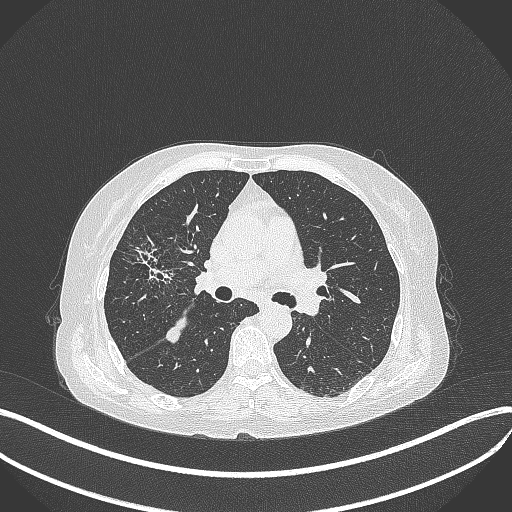
Chest CT, one axial slice; 120 kVp; lung window (W 1500 / L -600 HU); 1 mm slice thickness; 512 × 512 image matrix. Female patient, age 69 years. From the clinical record (not read from this slice): clinical TNM (as recorded): T1b N3 M0.
Structures marked on this image (bounding box drawn by a radiologist):
- lung tumour (recorded histology: small cell carcinoma): box from (x=122, y=236) to (x=183, y=290) px